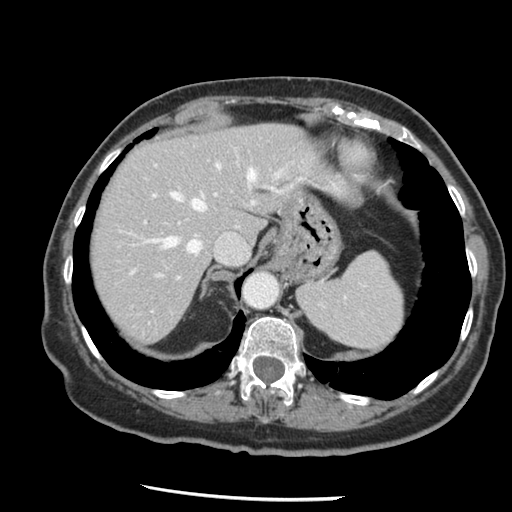
Contrast-enhanced abdominal CT, one axial slice. Position 105 of 148 along the scan axis. Reconstruction kernel STANDARD. Soft-tissue window (W 400 / L 40 HU). 2.5 mm slice thickness. 512 × 512 image matrix, field of view 330 × 330 mm. Female patient, age 85 years. From the clinical record (not read from this slice): diagnosis: colorectal cancer liver metastases, imaged before liver resection; multiple liver metastases: no; largest metastasis: 0.9 cm.
Outlined on this slice (manually delineated by an expert):
- hepatic veins: box from (x=132, y=164) to (x=288, y=273) px
- liver: (x=91, y=124)–(x=325, y=342)
- planned liver remnant (the part of the liver to remain after resection): (x=91, y=124)–(x=325, y=342)
- portal vein (with intrahepatic branches): (x=144, y=159)–(x=279, y=280)